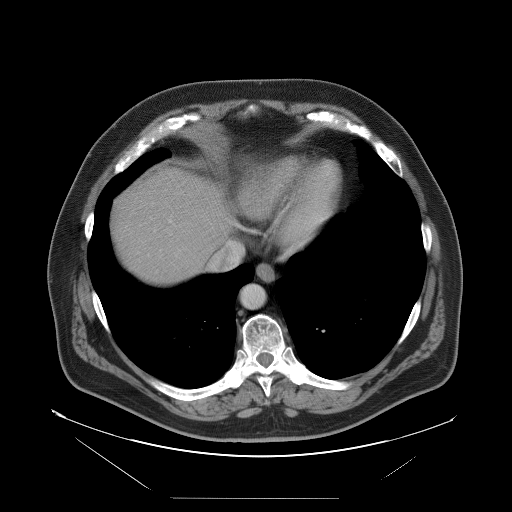
Contrast-enhanced abdominal CT, one axial slice. Position 91 of 114 along the scan axis. 120 kVp. Intravenous contrast given. Soft-tissue window (W 400 / L 40 HU). 512 × 512 image matrix. Male patient, age 61 years. From the clinical record (not read from this slice): diagnosis: colorectal cancer liver metastases, imaged before liver resection; multiple liver metastases: no; largest metastasis: 6.5 cm; disease in both lobes: yes.
Outlined on this slice (outlined manually by an expert reader):
- hepatic veins: bounding box (x1, y1, x2, y2) in pixels: (209, 241, 243, 269)
- liver: (111, 170, 234, 283)
- planned liver remnant (the part of the liver to remain after resection): (161, 170, 235, 249)